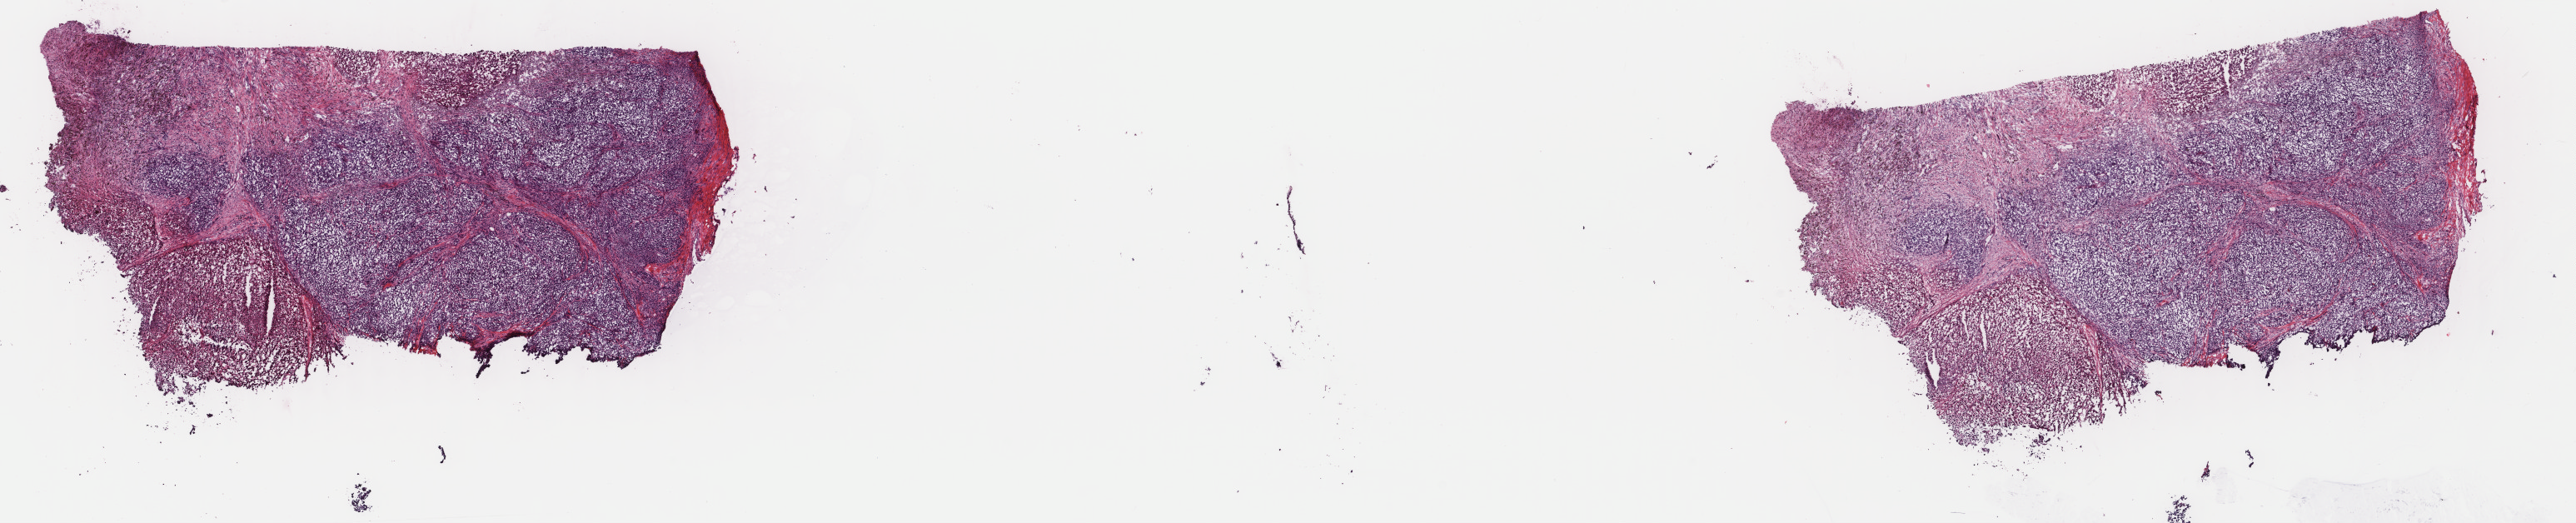
H&E-stained whole-slide image, whole scanned area (about 24.6 x 5.0 mm) shown as a low-resolution overview. Frozen section. Metastatic tumour sample, sampled site not recorded. Patient: male, age at initial diagnosis 80 years. Slide review estimates, as recorded: tumour cells 60%, tumour nuclei 75%, normal cells 0%, stromal cells 20%, necrosis 20%. Infiltration values recorded for this section: lymphocyte infiltration 0%, monocyte infiltration 0%, neutrophil infiltration 0%.
* this section: metastatic tumour tissue
* patient diagnosis: Malignant melanoma, NOS